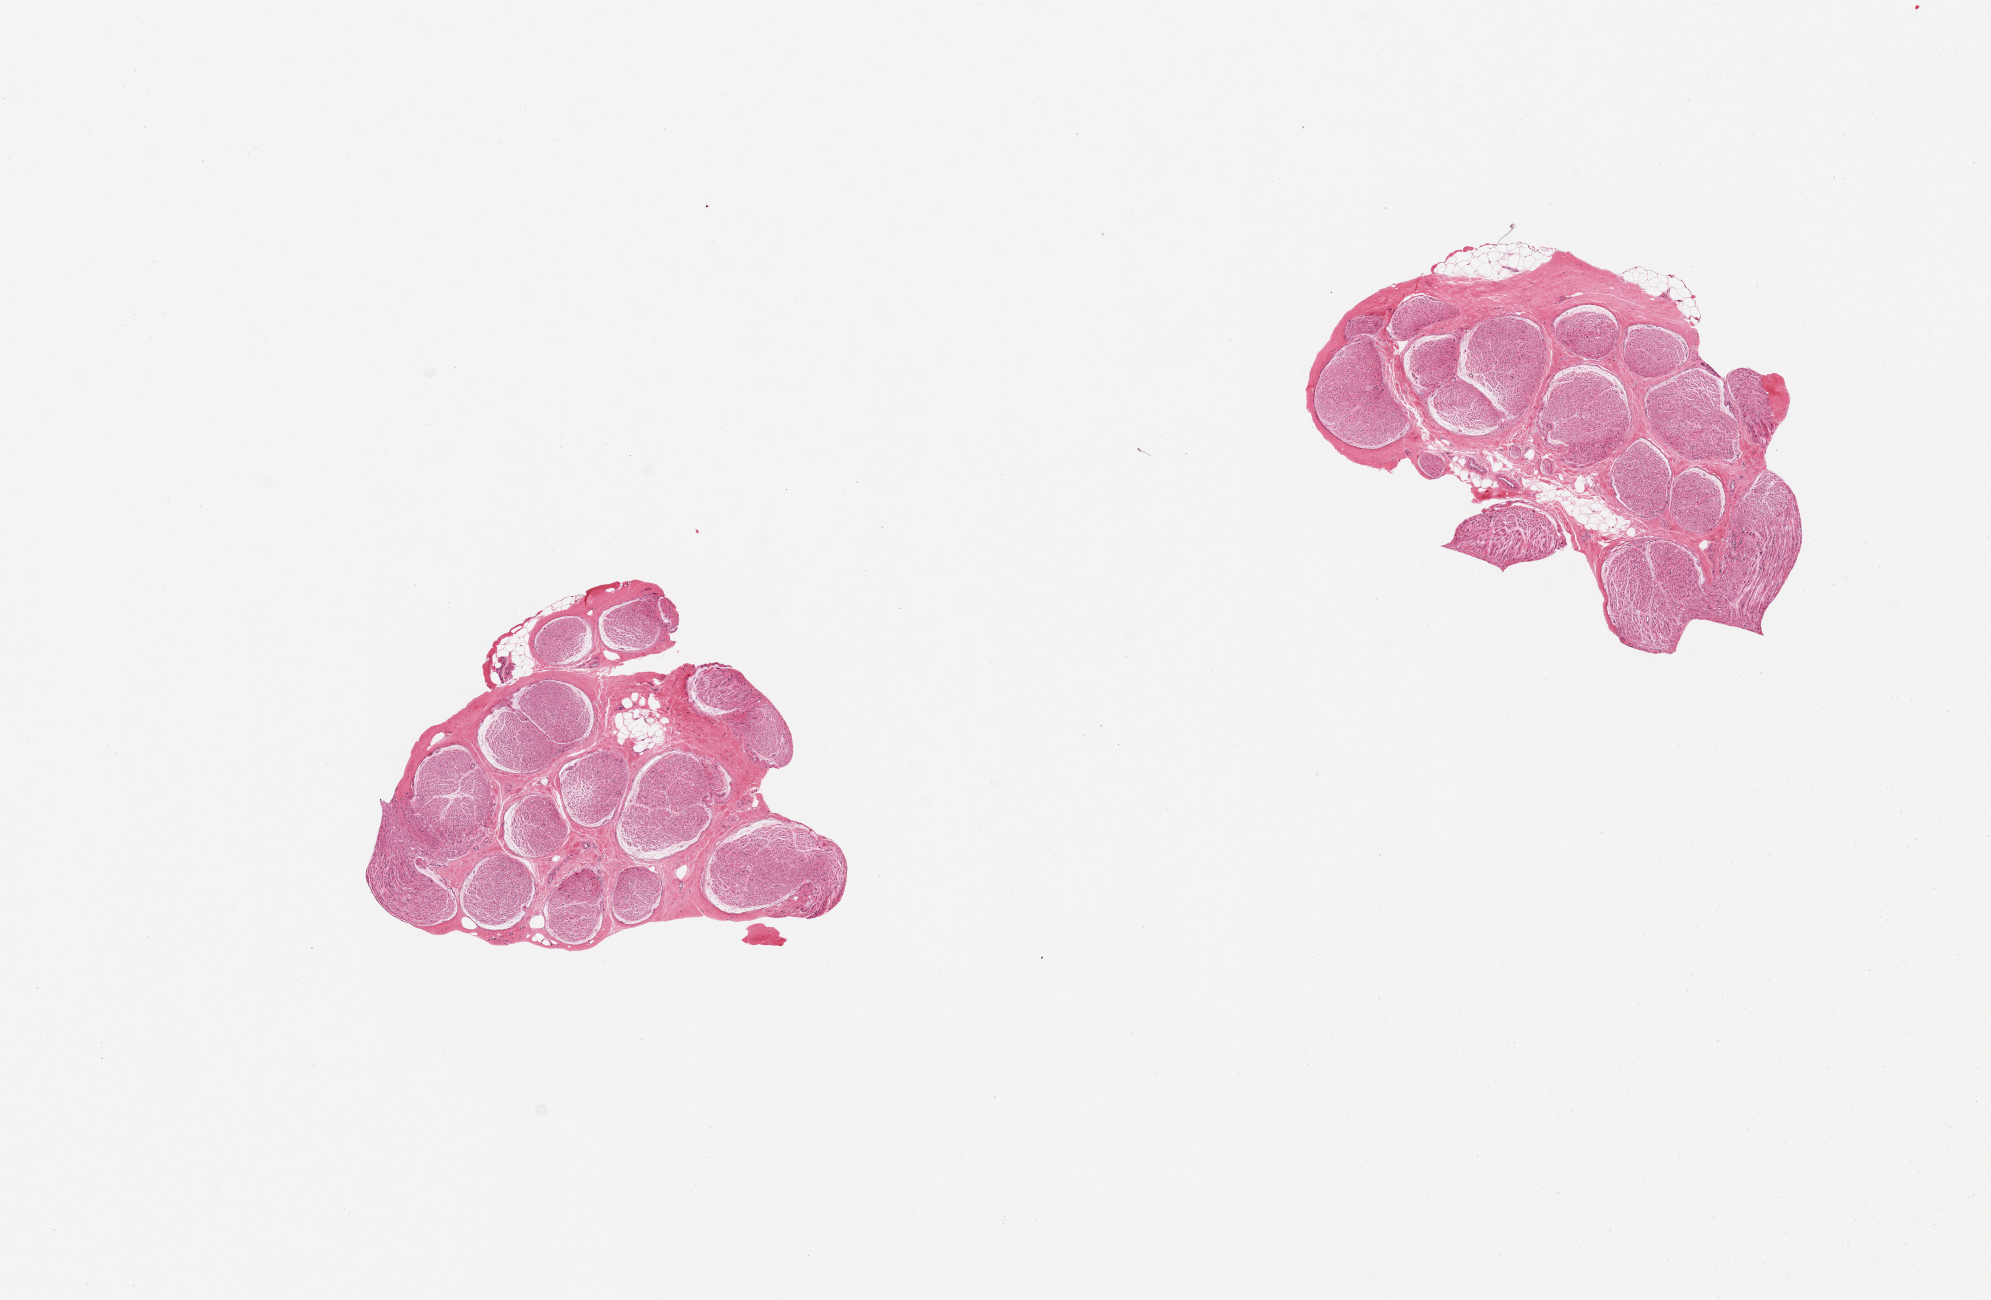
Whole-slide image, hematoxylin and eosin (H&E) stain — low-resolution overview of the scanned area, about 15.8 x 10.3 mm. PAXgene-fixed, paraffin-embedded tissue. Sampled site (target tissue): tibial nerve. Tissue donor sample. Male donor.
• reviewer comment on this tissue sample: 2 pieces, includes minimal portion of internal and attached fat (<10%)